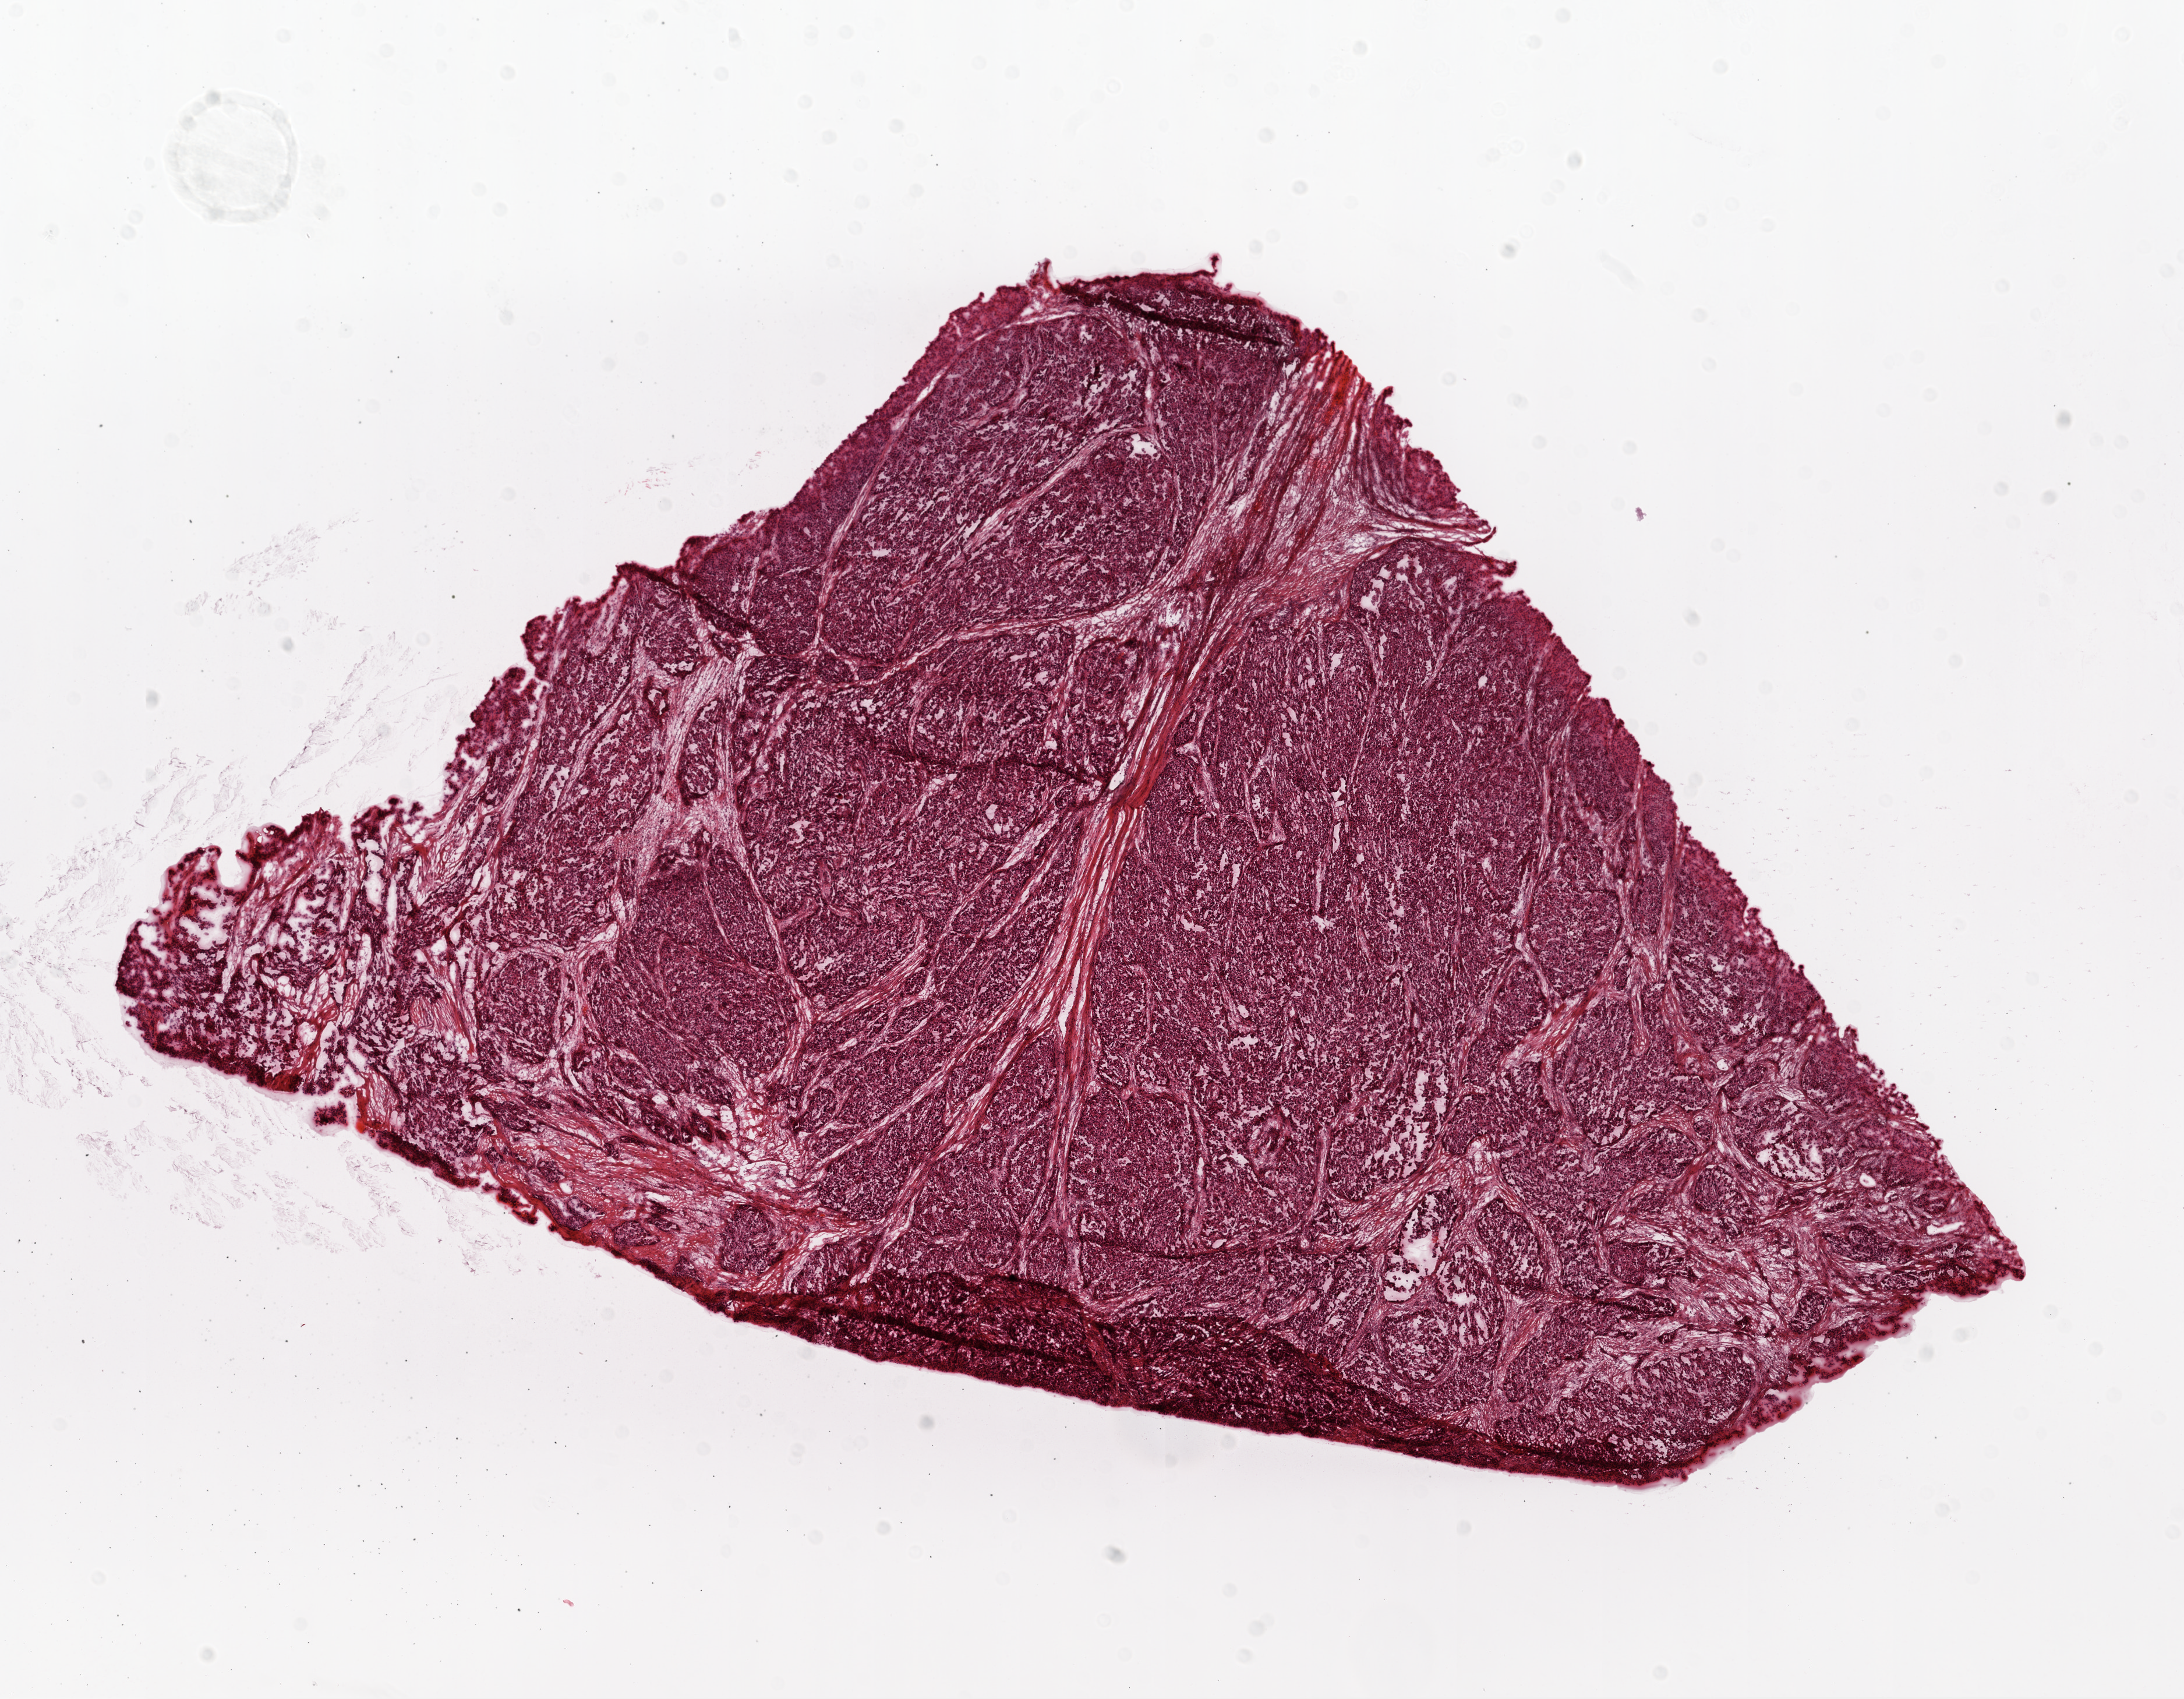
Whole-slide histology image, H&E — a low-resolution overview of the entire scanned area, about 15.0 x 11.7 mm (acquisition: 20x scan), frozen section from the top of the tissue portion, primary tumour sample from the ovary. Female patient; age at initial diagnosis 79 years. Composition of this section per pathologist review: tumour cells 85%, tumour nuclei 80%.
Histologic diagnosis: Serous cystadenocarcinoma, NOS.